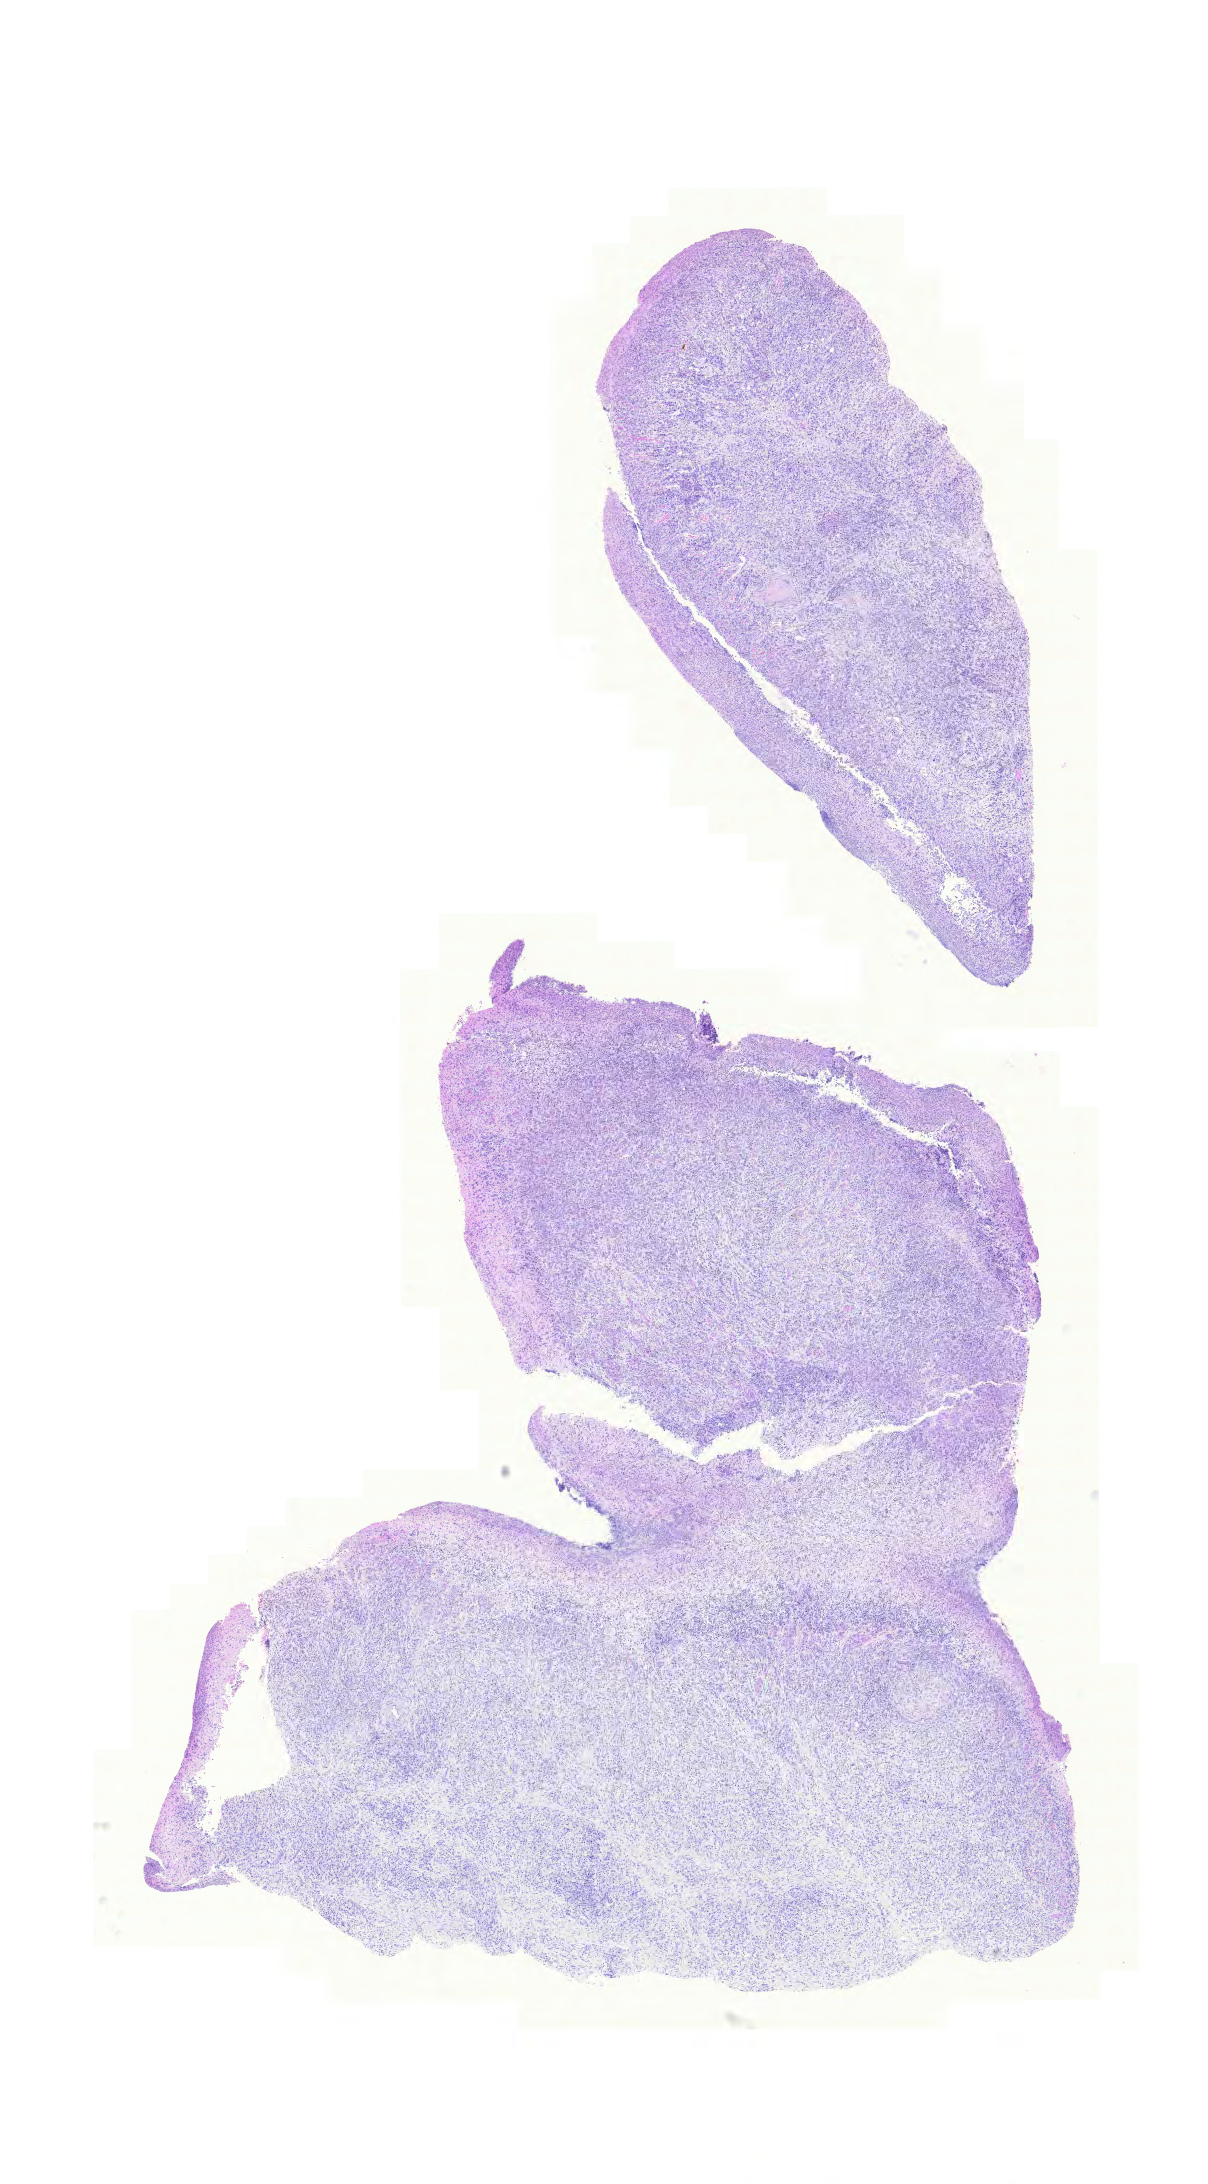
Whole-slide histology image, H&E, low-resolution overview of the scanned area, about 9.0 x 16.2 mm (acquisition: 20x scan); formalin-fixed paraffin-embedded (FFPE) diagnostic section; stomach, primary tumour sample. Patient: female, age at initial diagnosis 72 years. Histologic grade: G3 (poorly differentiated).
AJCC pathologic stage: IV (6th edition). Lymph nodes positive (case pathology): 25 of 25 examined. Diagnosis: Carcinoma, diffuse type.